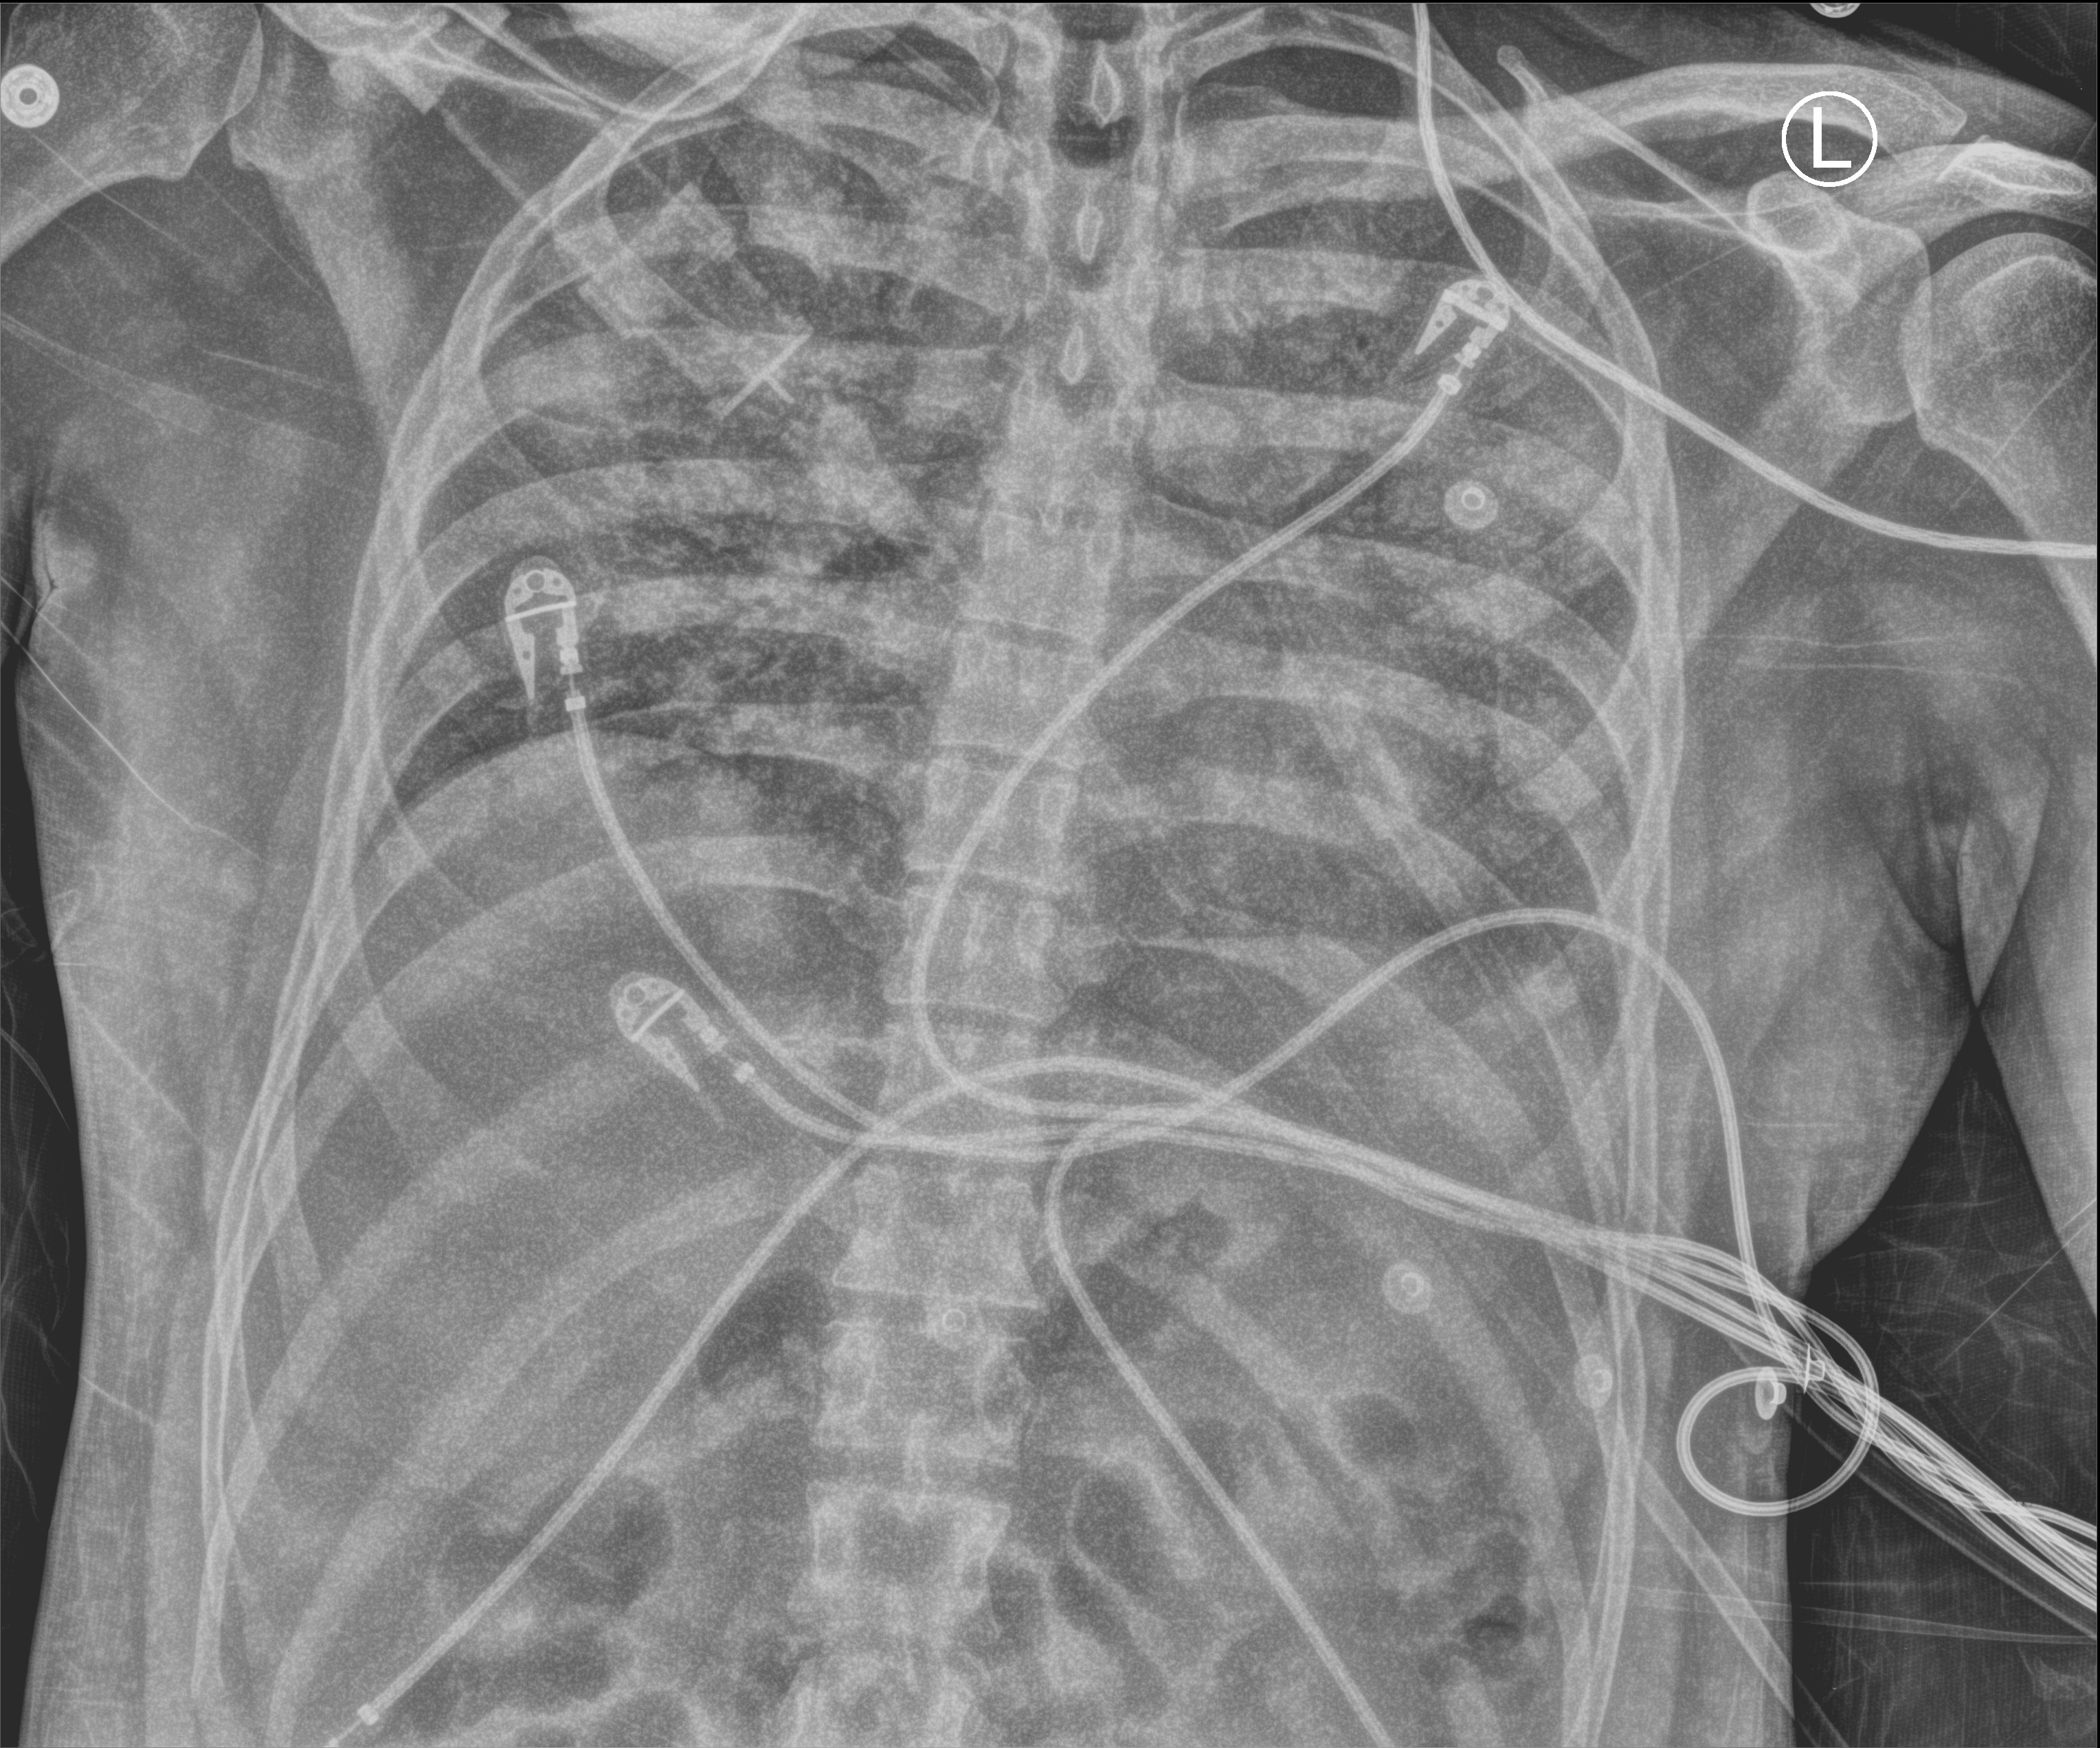
Chest X-ray (portable); anteroposterior (AP) projection. Patient hospitalised with COVID-19; male, aged 18–59 years.
Hospital-stay facts (about this admission, not read from this image; timing relative to this image not recorded): admitted to intensive care during this hospital stay: yes.